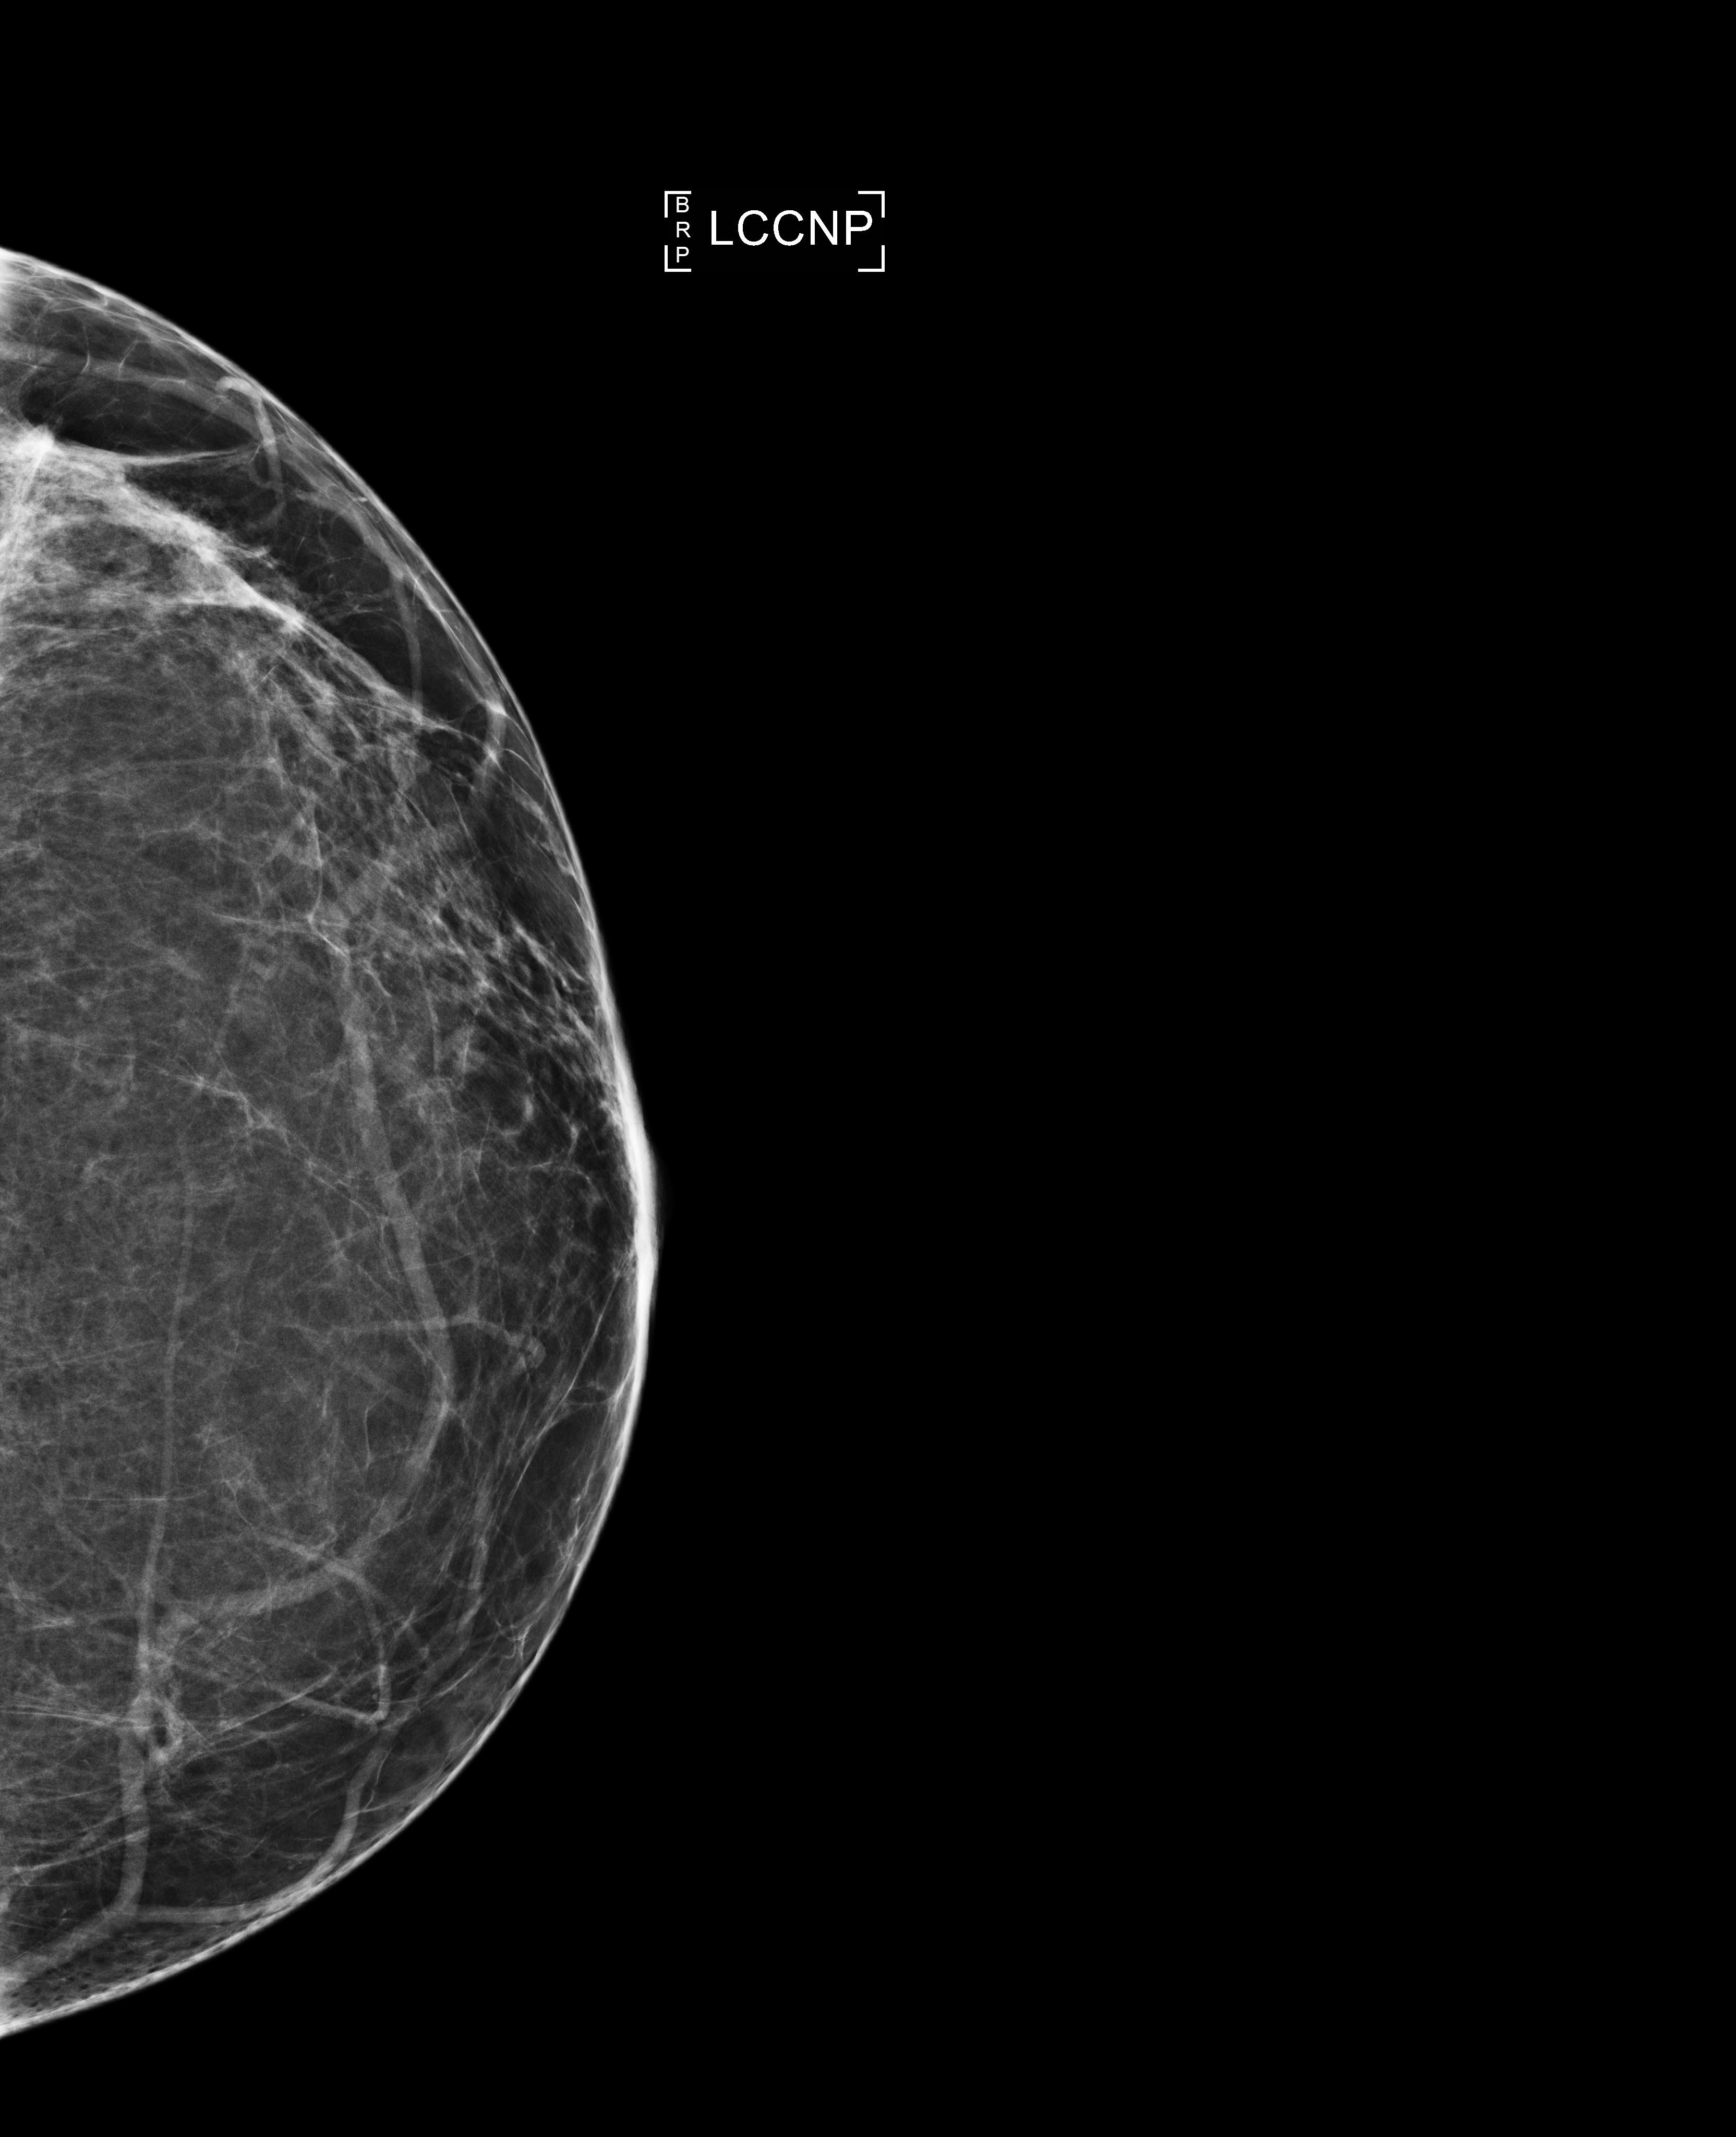
Screening examination. Patient: female, 51 years.
Image type: full-field digital mammogram. Breast: left. Projection: craniocaudal (CC) view, nipple in profile.